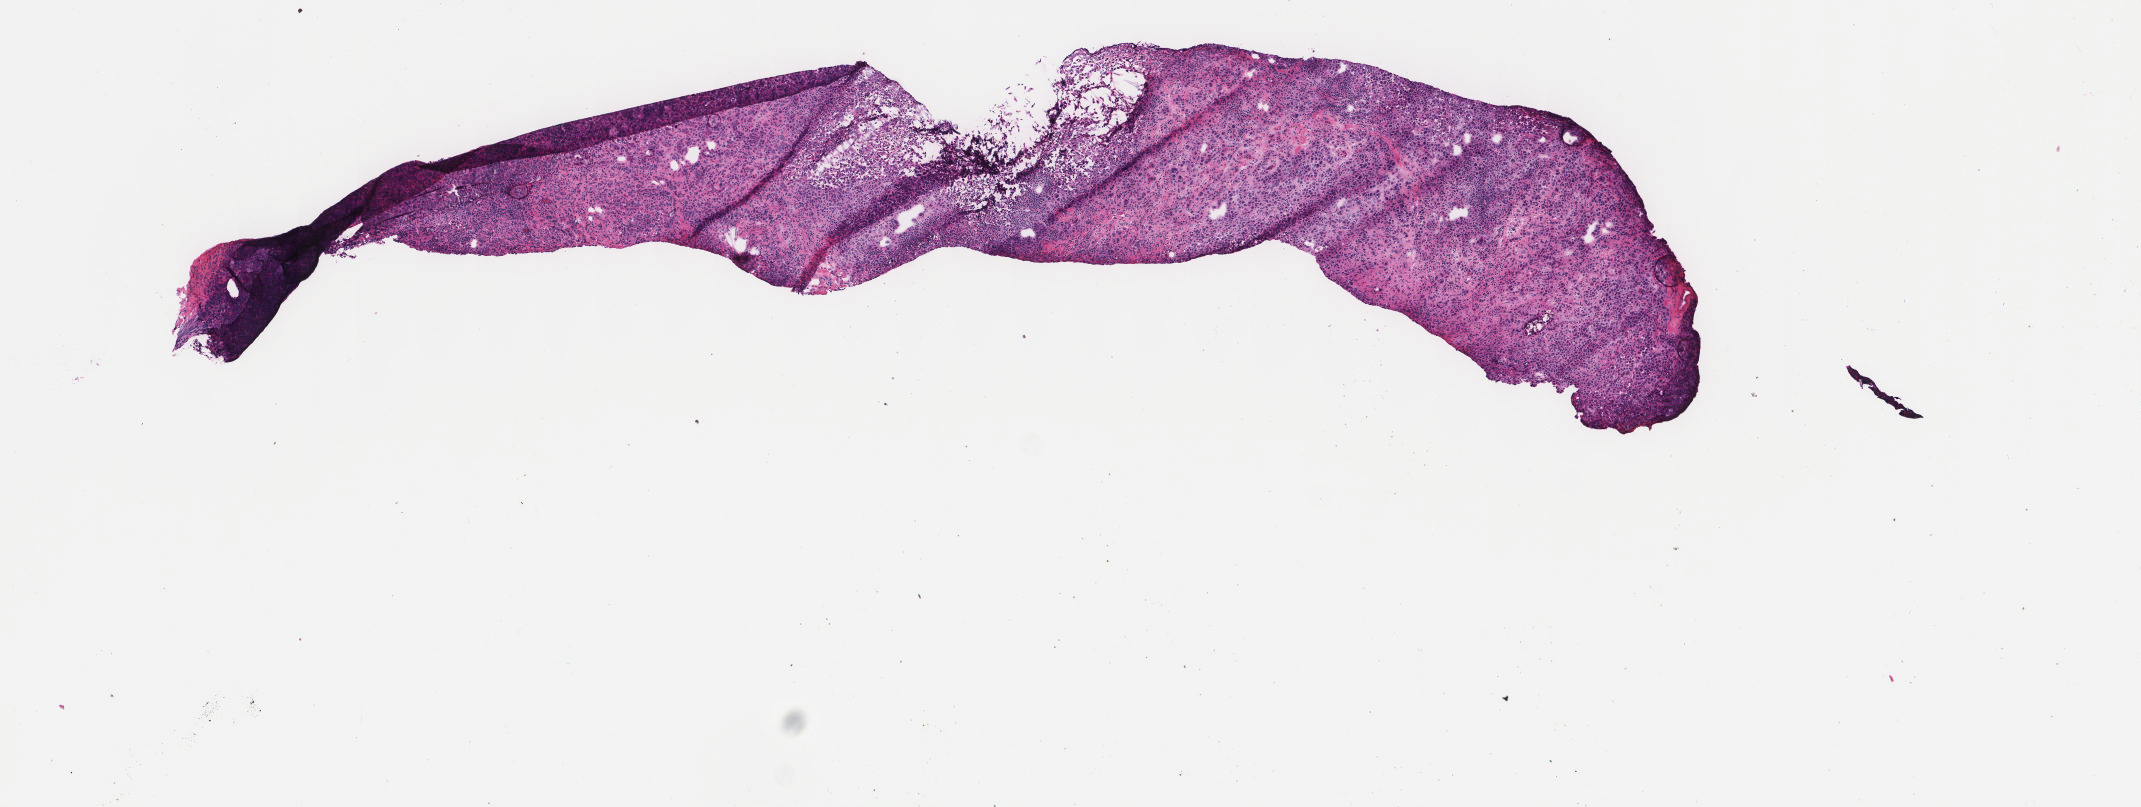
H&E whole-slide image — shown as a low-resolution overview of the whole scanned area (about 8.5 x 3.2 mm); frozen section from the top of the tissue portion; sample: primary tumour, breast. Female, age 50 years at initial diagnosis.
Pathologic diagnosis: Infiltrating duct and lobular carcinoma.